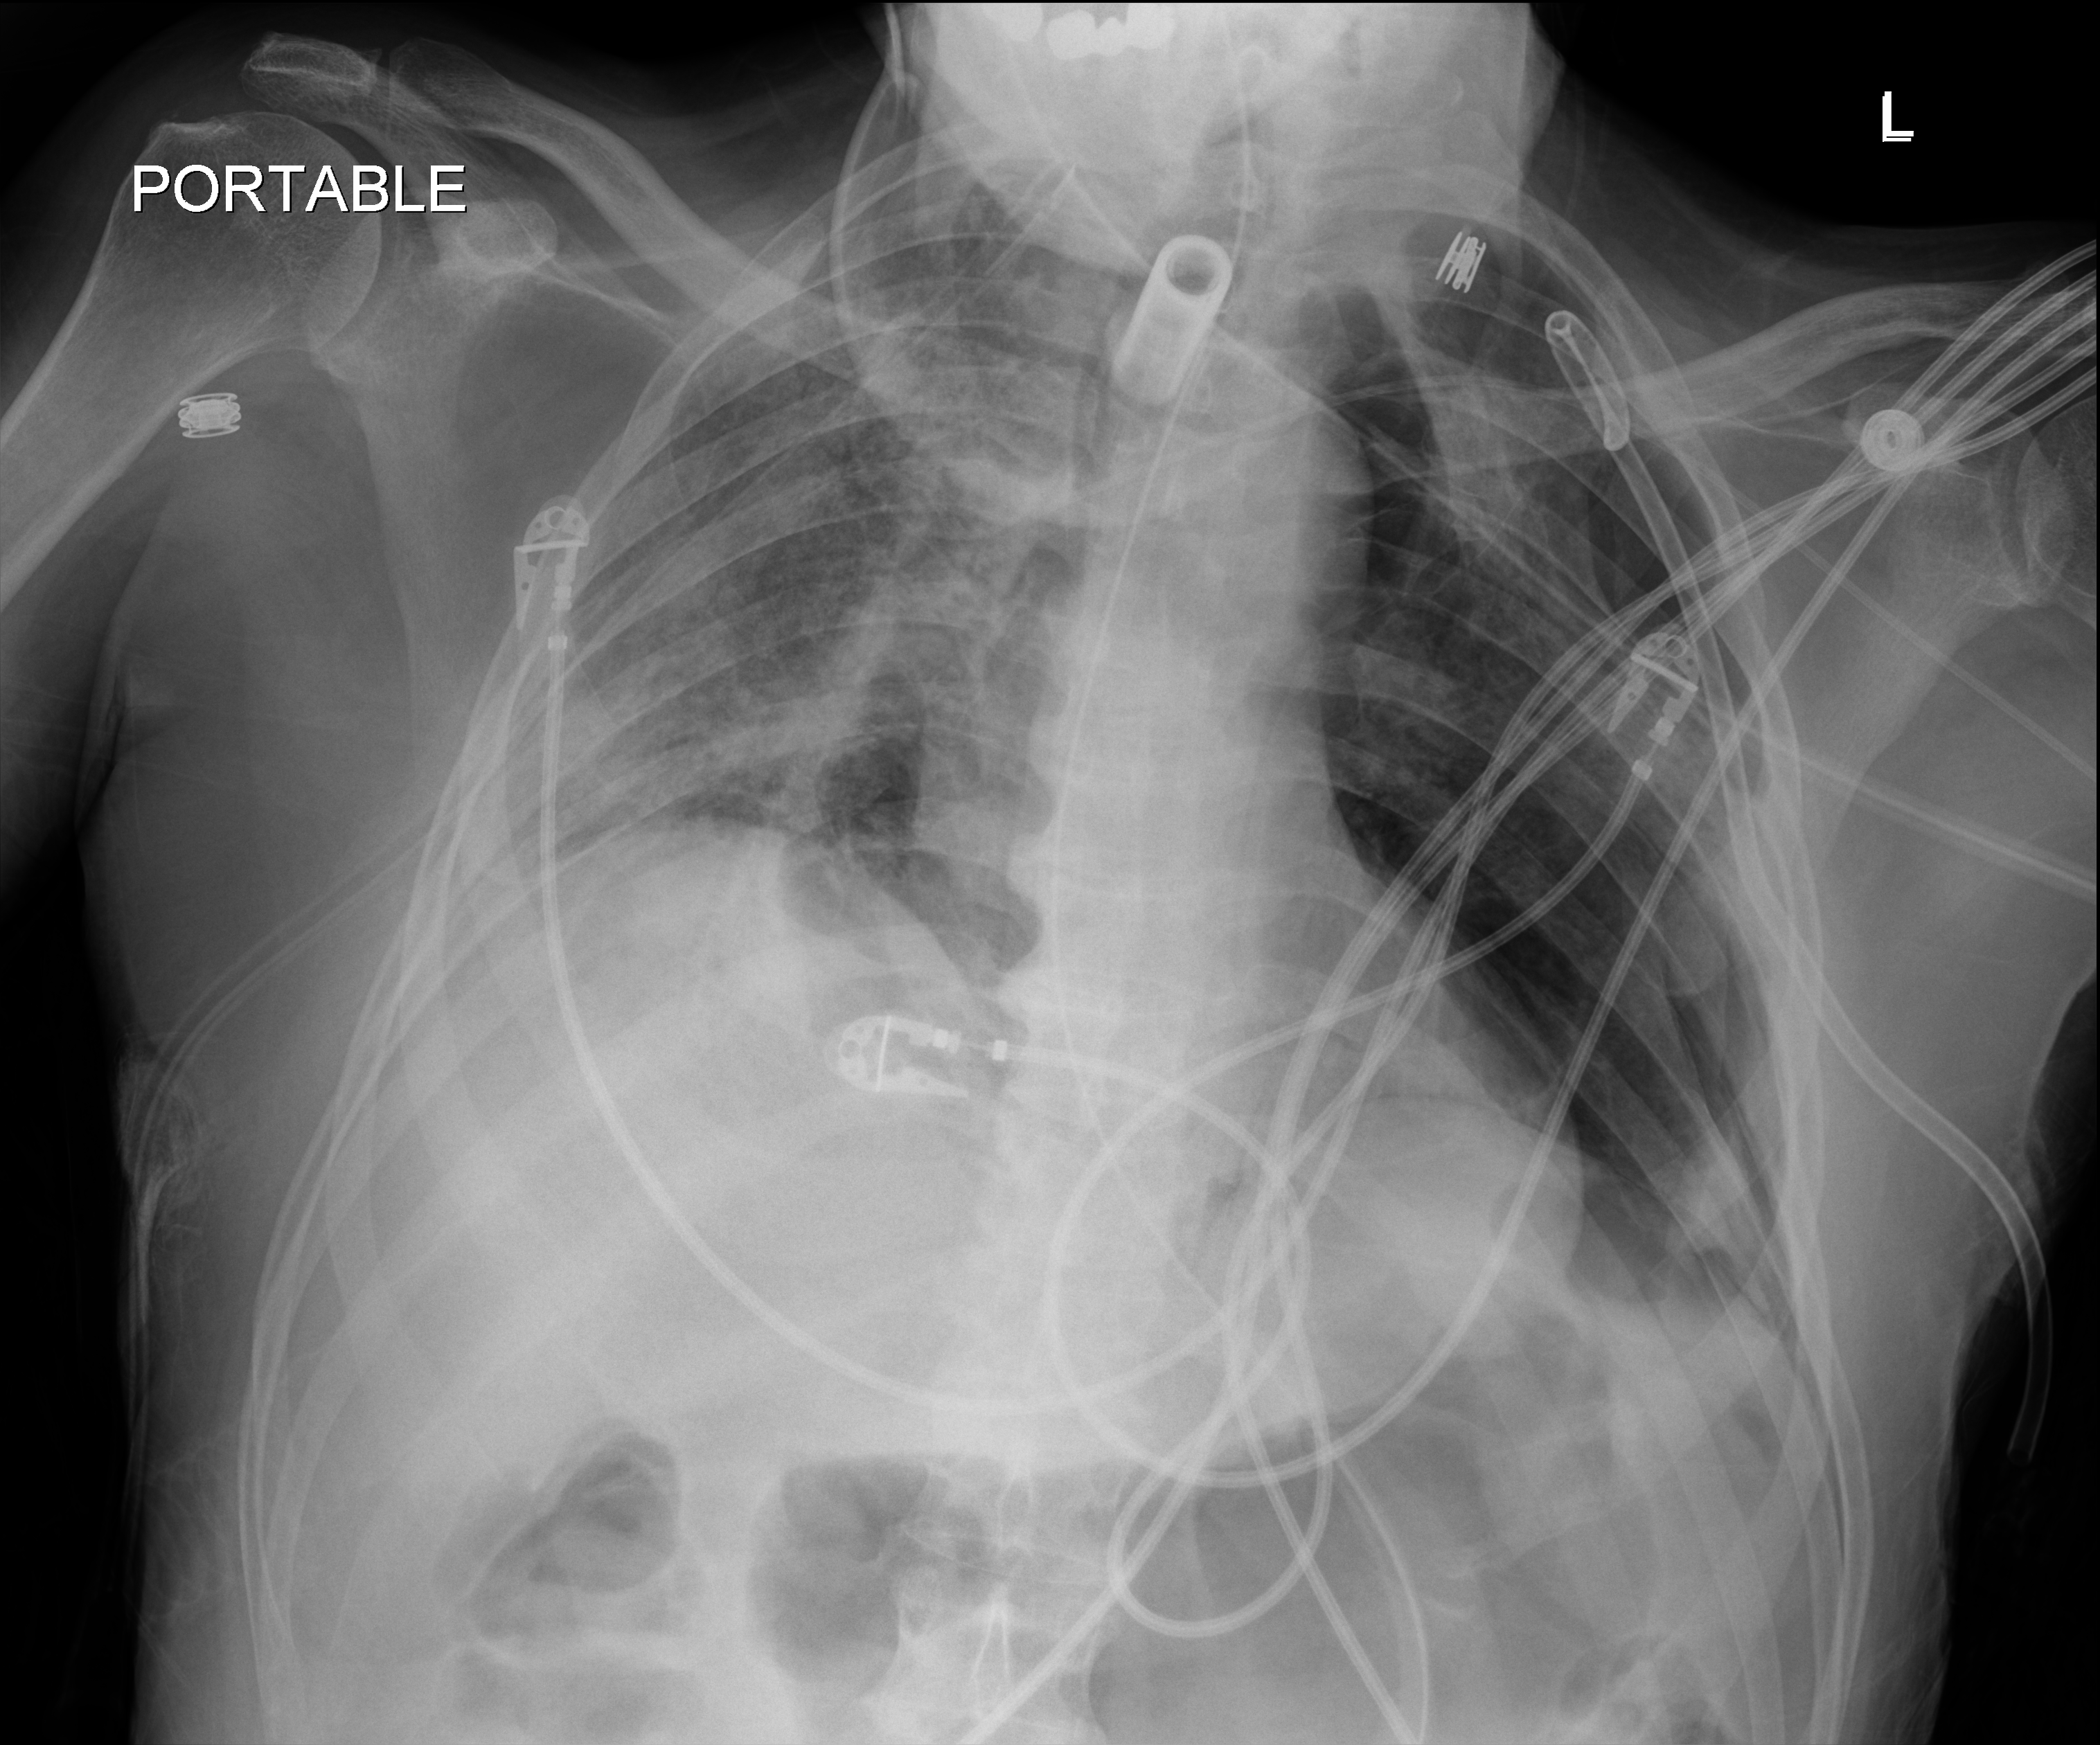
Portable chest radiograph, anteroposterior (AP) projection. Male patient hospitalised with COVID-19, age 18–59 years.
From the hospital-stay record, not from the radiograph (when in the stay this image was taken is not recorded):
- admitted to intensive care during this hospital stay: yes